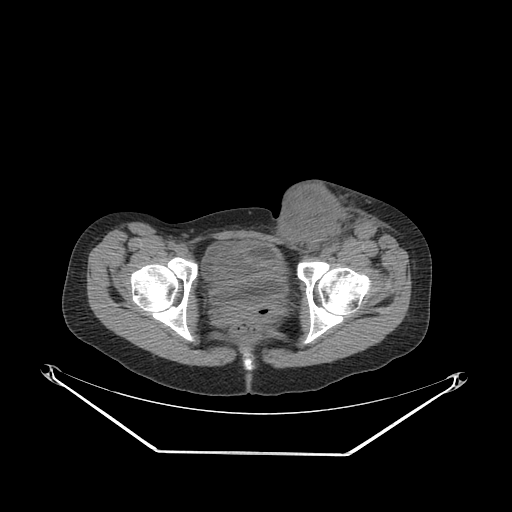
CT of an extremity soft-tissue mass (from a PET/CT study), one axial slice. Position 70 of 267 along the scan axis. Soft-tissue window (W 400 / L 40 HU). 3.75 mm slice thickness. 512 × 512 image matrix. Female patient. From the clinical record (not read from this slice): histological type: leiomyosarcoma; grade: high; site of the primary tumour: groin.
Annotated regions visible in this slice (expert contour drawn on MRI and transferred to this co-registered scan by the dataset authors):
- gross tumour volume including surrounding oedema: bounding box <269,187,382,261> (left, top, right, bottom; pixels)
- gross tumour volume (mass): <269,189,346,254>